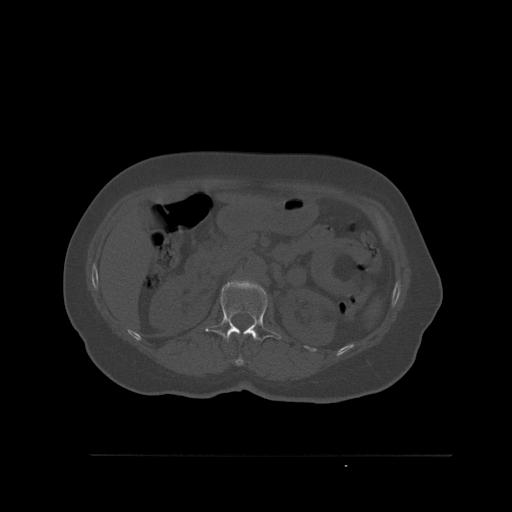
CT including the spine, one axial slice. Slice 266 of 527 in the series (ordered by position). Bone window (W 1800 / L 400 HU). 1.5 mm slice thickness. 512 × 512 image matrix. Female patient, age 73 years. Case-level facts recorded for this patient, not image findings: primary cancer: breast.
Outlined on this slice (semi-automatically segmented with operator editing):
- L1 vertebra: bounding box (x1, y1, x2, y2) in pixels: (205, 280, 281, 342)
- T12 vertebra: (228, 336, 244, 366)